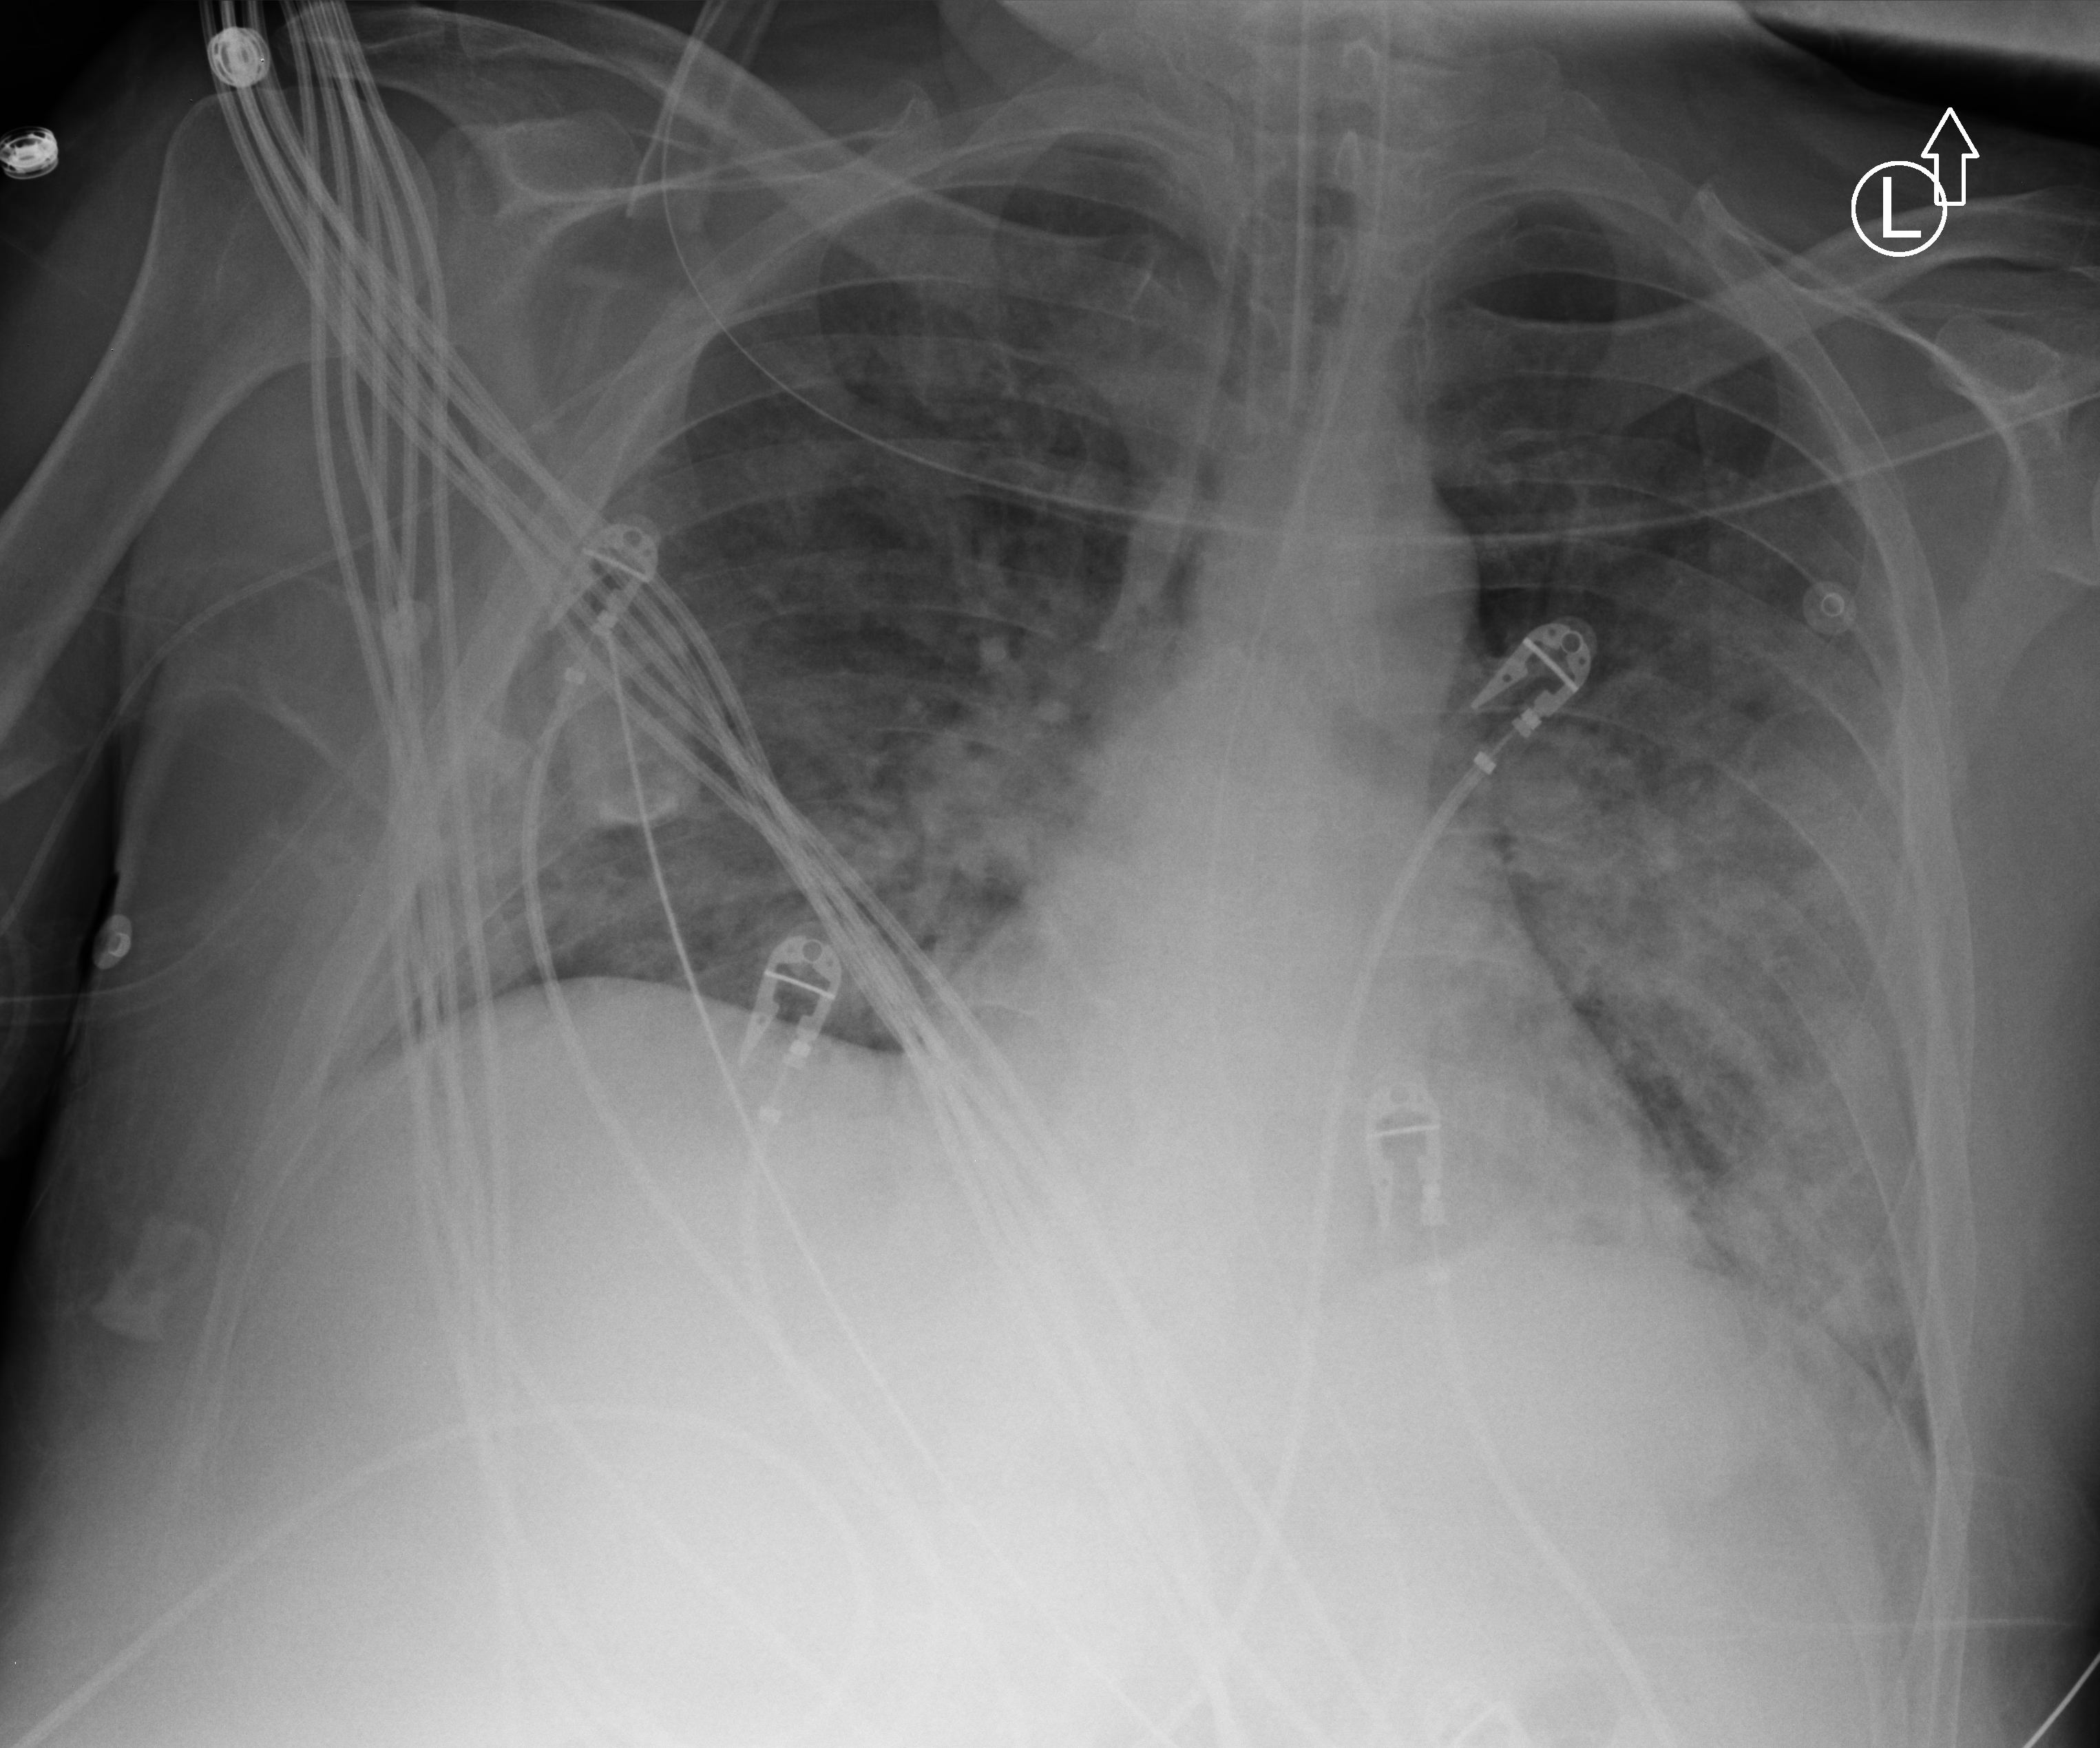
Bedside chest radiograph (computed radiography); anteroposterior (AP) projection. Male patient hospitalised with COVID-19, age 18–59 years.
Hospital-stay facts (about this admission, not read from this image; timing relative to this image not recorded): mechanically ventilated during this hospital stay: yes; admitted to intensive care during this hospital stay: yes.